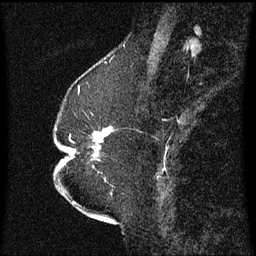
Breast MRI (dynamic contrast-enhanced), one sagittal slice. Dynamic contrast-enhanced series, image 2 of 3 at this slice position (ordered by acquisition). 1.5 T. TE 4.2 ms, TR 8.4 ms. 2.3 mm slice thickness. 256 × 256 image matrix, field of view 200 × 200 mm. Female patient, age 52 years. From the clinical record (not read from this slice): setting: breast cancer imaged before/during neoadjuvant chemotherapy; receptor status: HR-positive, HER2-negative.
Structures marked on this image (semi-automatically segmented with operator editing):
- analysis volume of interest (the breast-tissue region the enhancement analysis was run in; not a lesion): box from (x=65, y=128) to (x=114, y=183) px
- tumour enhancement mask (voxels above the 70 % enhancement threshold inside the analysis volume of interest): (x=93, y=128)–(x=113, y=157)